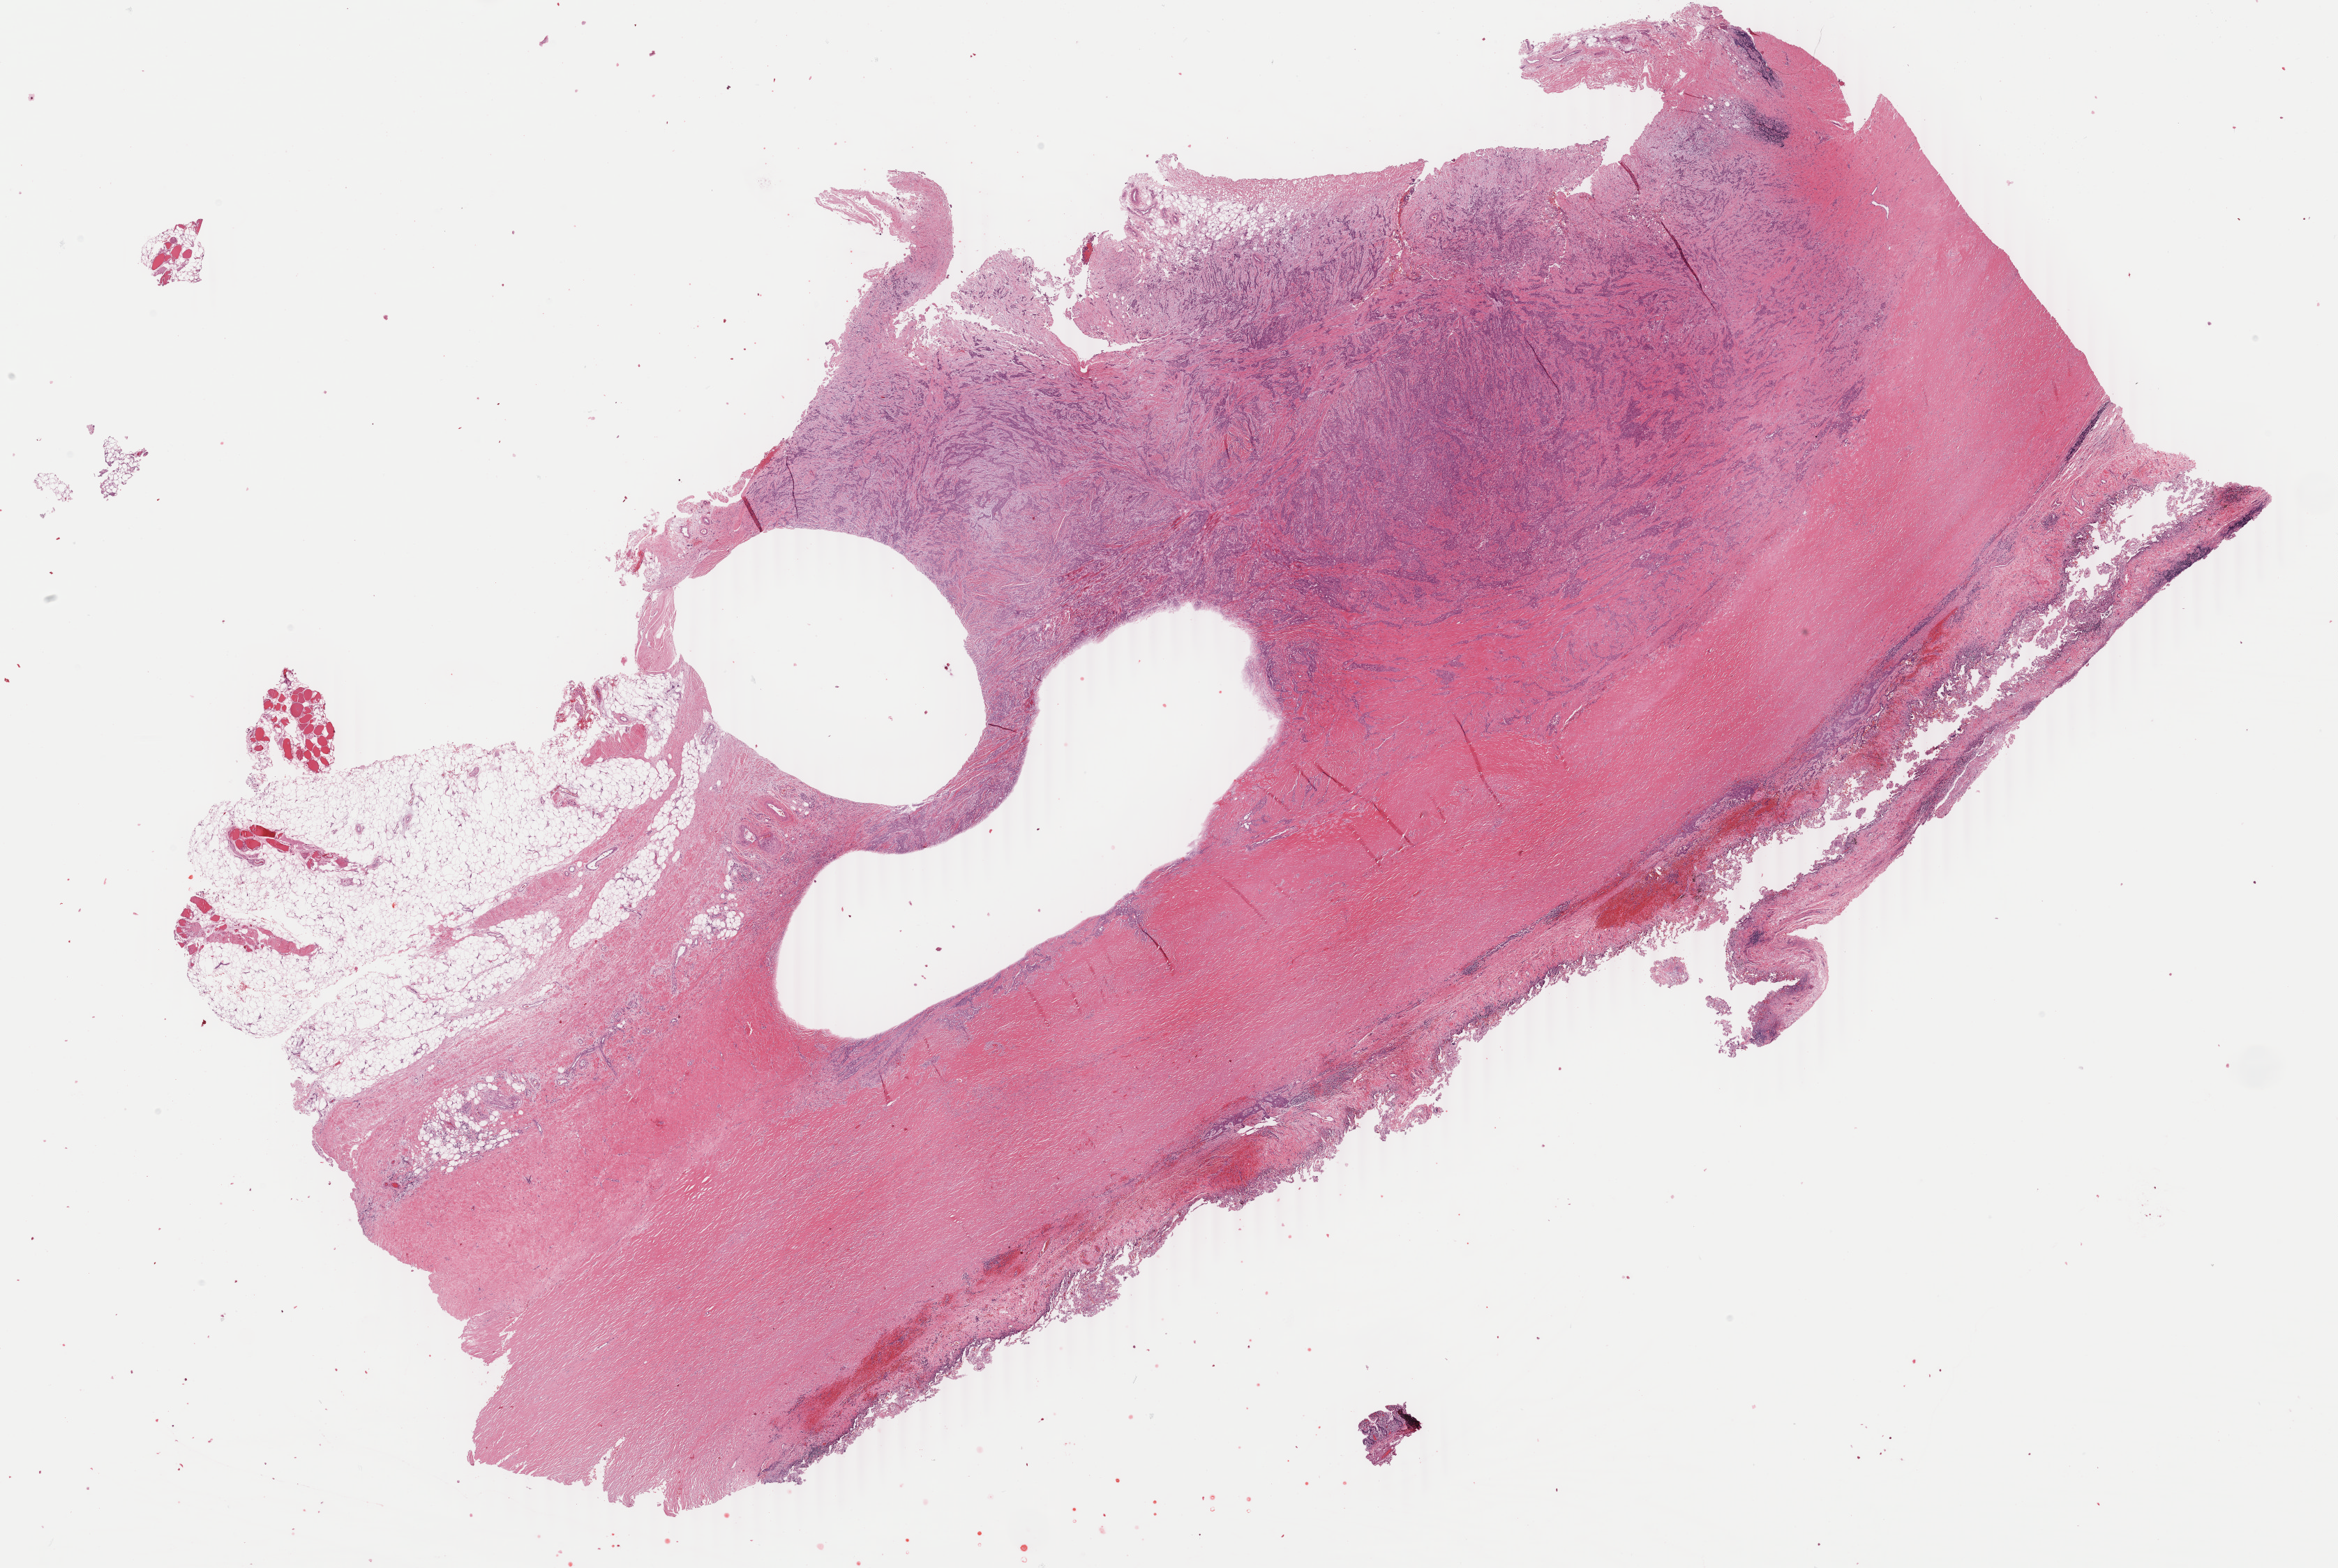
Digitized H&E tissue section (whole slide) — shown as a low-resolution overview of the whole scanned area (about 26.7 x 17.9 mm), formalin-fixed paraffin-embedded (FFPE) diagnostic section, sample: primary tumour, mesothelium. Patient: male, age at initial diagnosis 75 years.
- TNM: T2 N0 M0
- pathologic diagnosis: Epithelioid mesothelioma, malignant
- AJCC pathologic stage: II (6th edition)